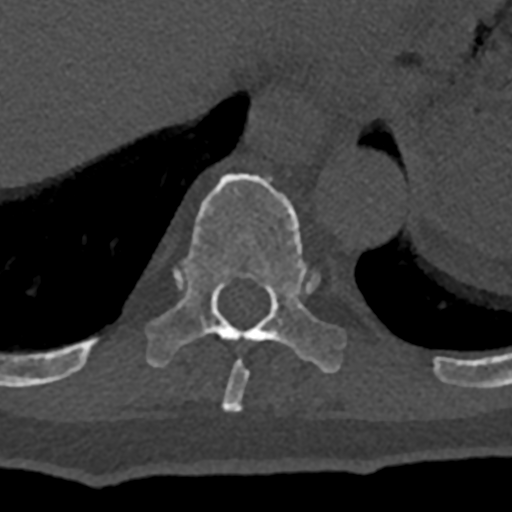
CT including the spine, one axial slice; position 610 of 797 along the scan axis; reconstruction kernel Br40s/3; 120 kVp; bone window (W 1800 / L 400 HU); 512 × 512 image matrix, field of view 160 × 160 mm. Male patient, age 74 years. Case-level facts recorded for this patient, not image findings: primary cancer: renal; vertebrae with lytic lesions (as recorded): T10, L1, L2, L3, L4, L5.
Structures marked on this image (semi-automatically segmented with operator editing):
- T10 vertebra: bounding box <70,173,346,375> (left, top, right, bottom; pixels)
- T9 vertebra: <222,360,249,412>